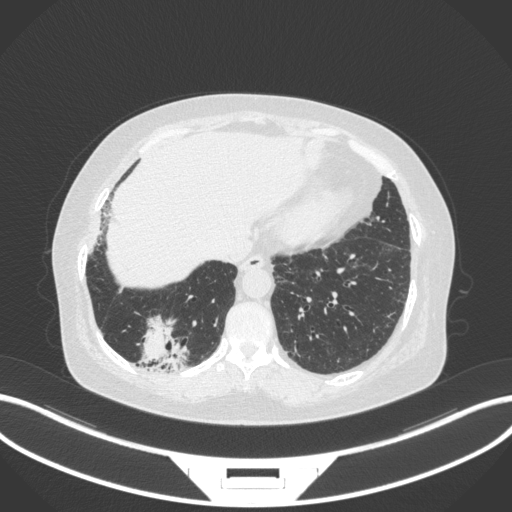
Chest CT, one axial slice. Slice 40 of 303 in the series (ordered by position). Reconstruction kernel B31f. 120 kVp. Lung window (W 1500 / L -600 HU). 512 × 512 image matrix. Patient: female, 65 years. Case-level facts recorded for this patient, not image findings: clinical TNM (as recorded): T2b N1 M0; histopathological grade: G1.
Outlined on this slice (rectangle marked by the reading radiologist):
- lung tumour (recorded histology: adenocarcinoma): bounding box <135,314,189,371> (left, top, right, bottom; pixels)